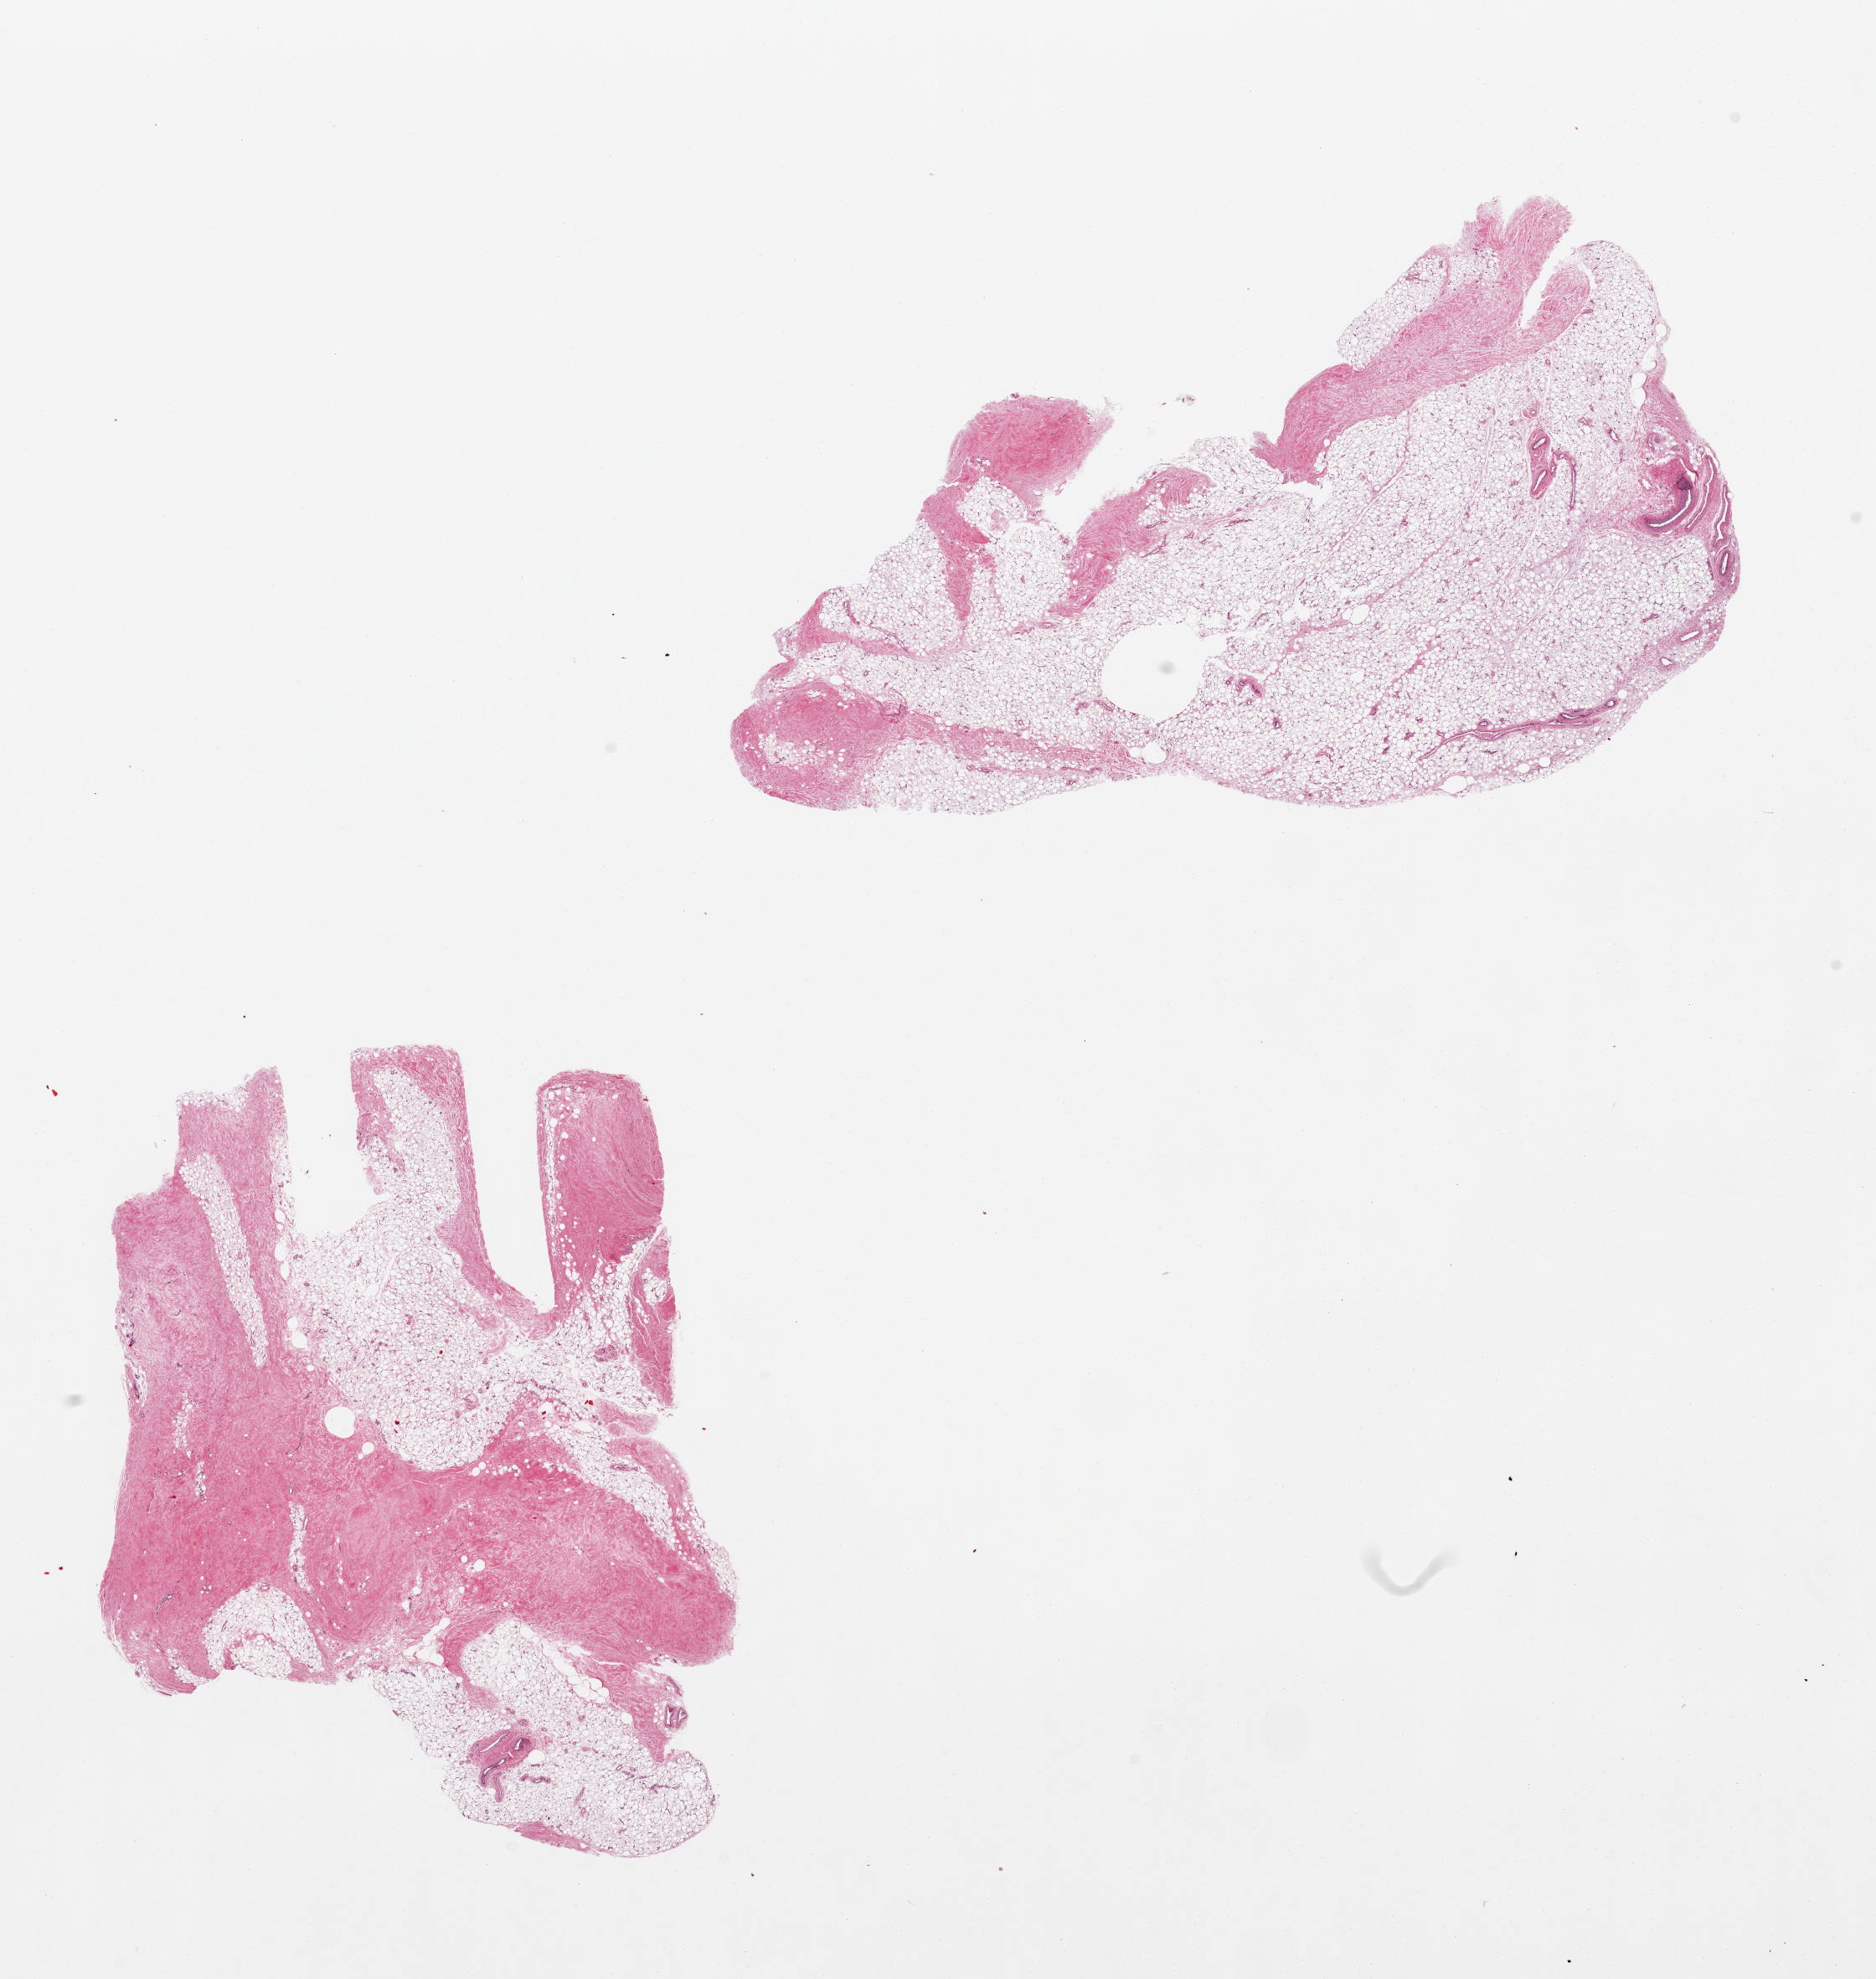
Haematoxylin and eosin whole-slide image, low-resolution overview of the scanned area, about 17.7 x 18.7 mm; PAXgene-fixed paraffin-embedded (PFPE) section; target tissue: breast; tissue donor sample. Donor: male.
- pathologist's review note for this sample: 2 pieces; ~25% is fibrovascular tissue, no ductal elements